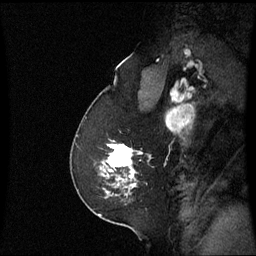
Breast MRI (dynamic contrast-enhanced), one sagittal slice; slice 43 of 60 in the series (ordered by position); dynamic contrast-enhanced series, image 2 of 3 at this slice position (ordered by acquisition); 1.5 T; TE 4.2 ms, TR 8.9 ms; 2.2 mm slice thickness; 256 × 256 image matrix. Patient: female, 58 years. Case-level facts recorded for this patient, not image findings: setting: breast cancer imaged before/during neoadjuvant chemotherapy; receptor status: triple-negative.
Outlined on this slice (semi-automatically segmented with operator editing):
- analysis volume of interest (the breast-tissue region the enhancement analysis was run in; not a lesion): bounding box <100,140,151,193> (left, top, right, bottom; pixels)
- tumour enhancement mask (voxels above the 70 % enhancement threshold inside the analysis volume of interest): <108,144,137,187>